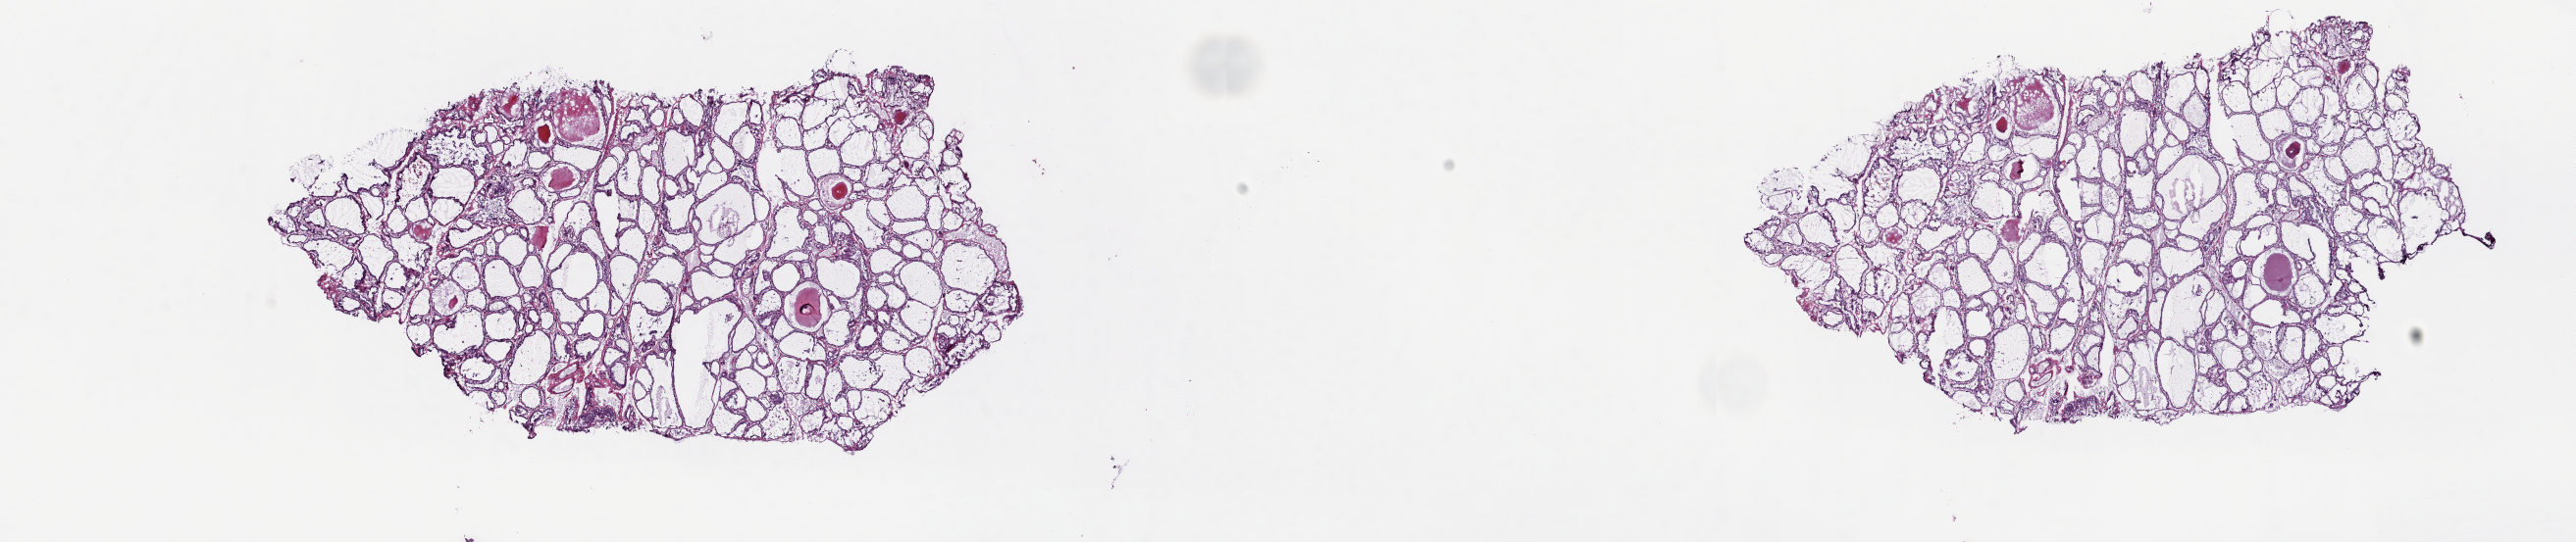
Whole-slide histology image, H&E-stained — shown as a low-resolution overview of the whole scanned area (about 20.8 x 4.4 mm, from a 20x scan). Frozen section from the top of the tissue portion. Thyroid, solid tissue normal (non-tumour tissue) sample. Patient: female, age at initial diagnosis 23 years. Pathologist review of this section (percent, as recorded): tumour cells 0%, tumour nuclei 0%, normal cells 100%, stromal cells 0%, necrosis 0%. Infiltration values recorded for this section: lymphocyte infiltration 0%, monocyte infiltration 0%, neutrophil infiltration 0%.
- this section: solid tissue normal (non-tumour) sample from the same patient
- patient diagnosis: Papillary carcinoma, follicular variant (thyroid gland)